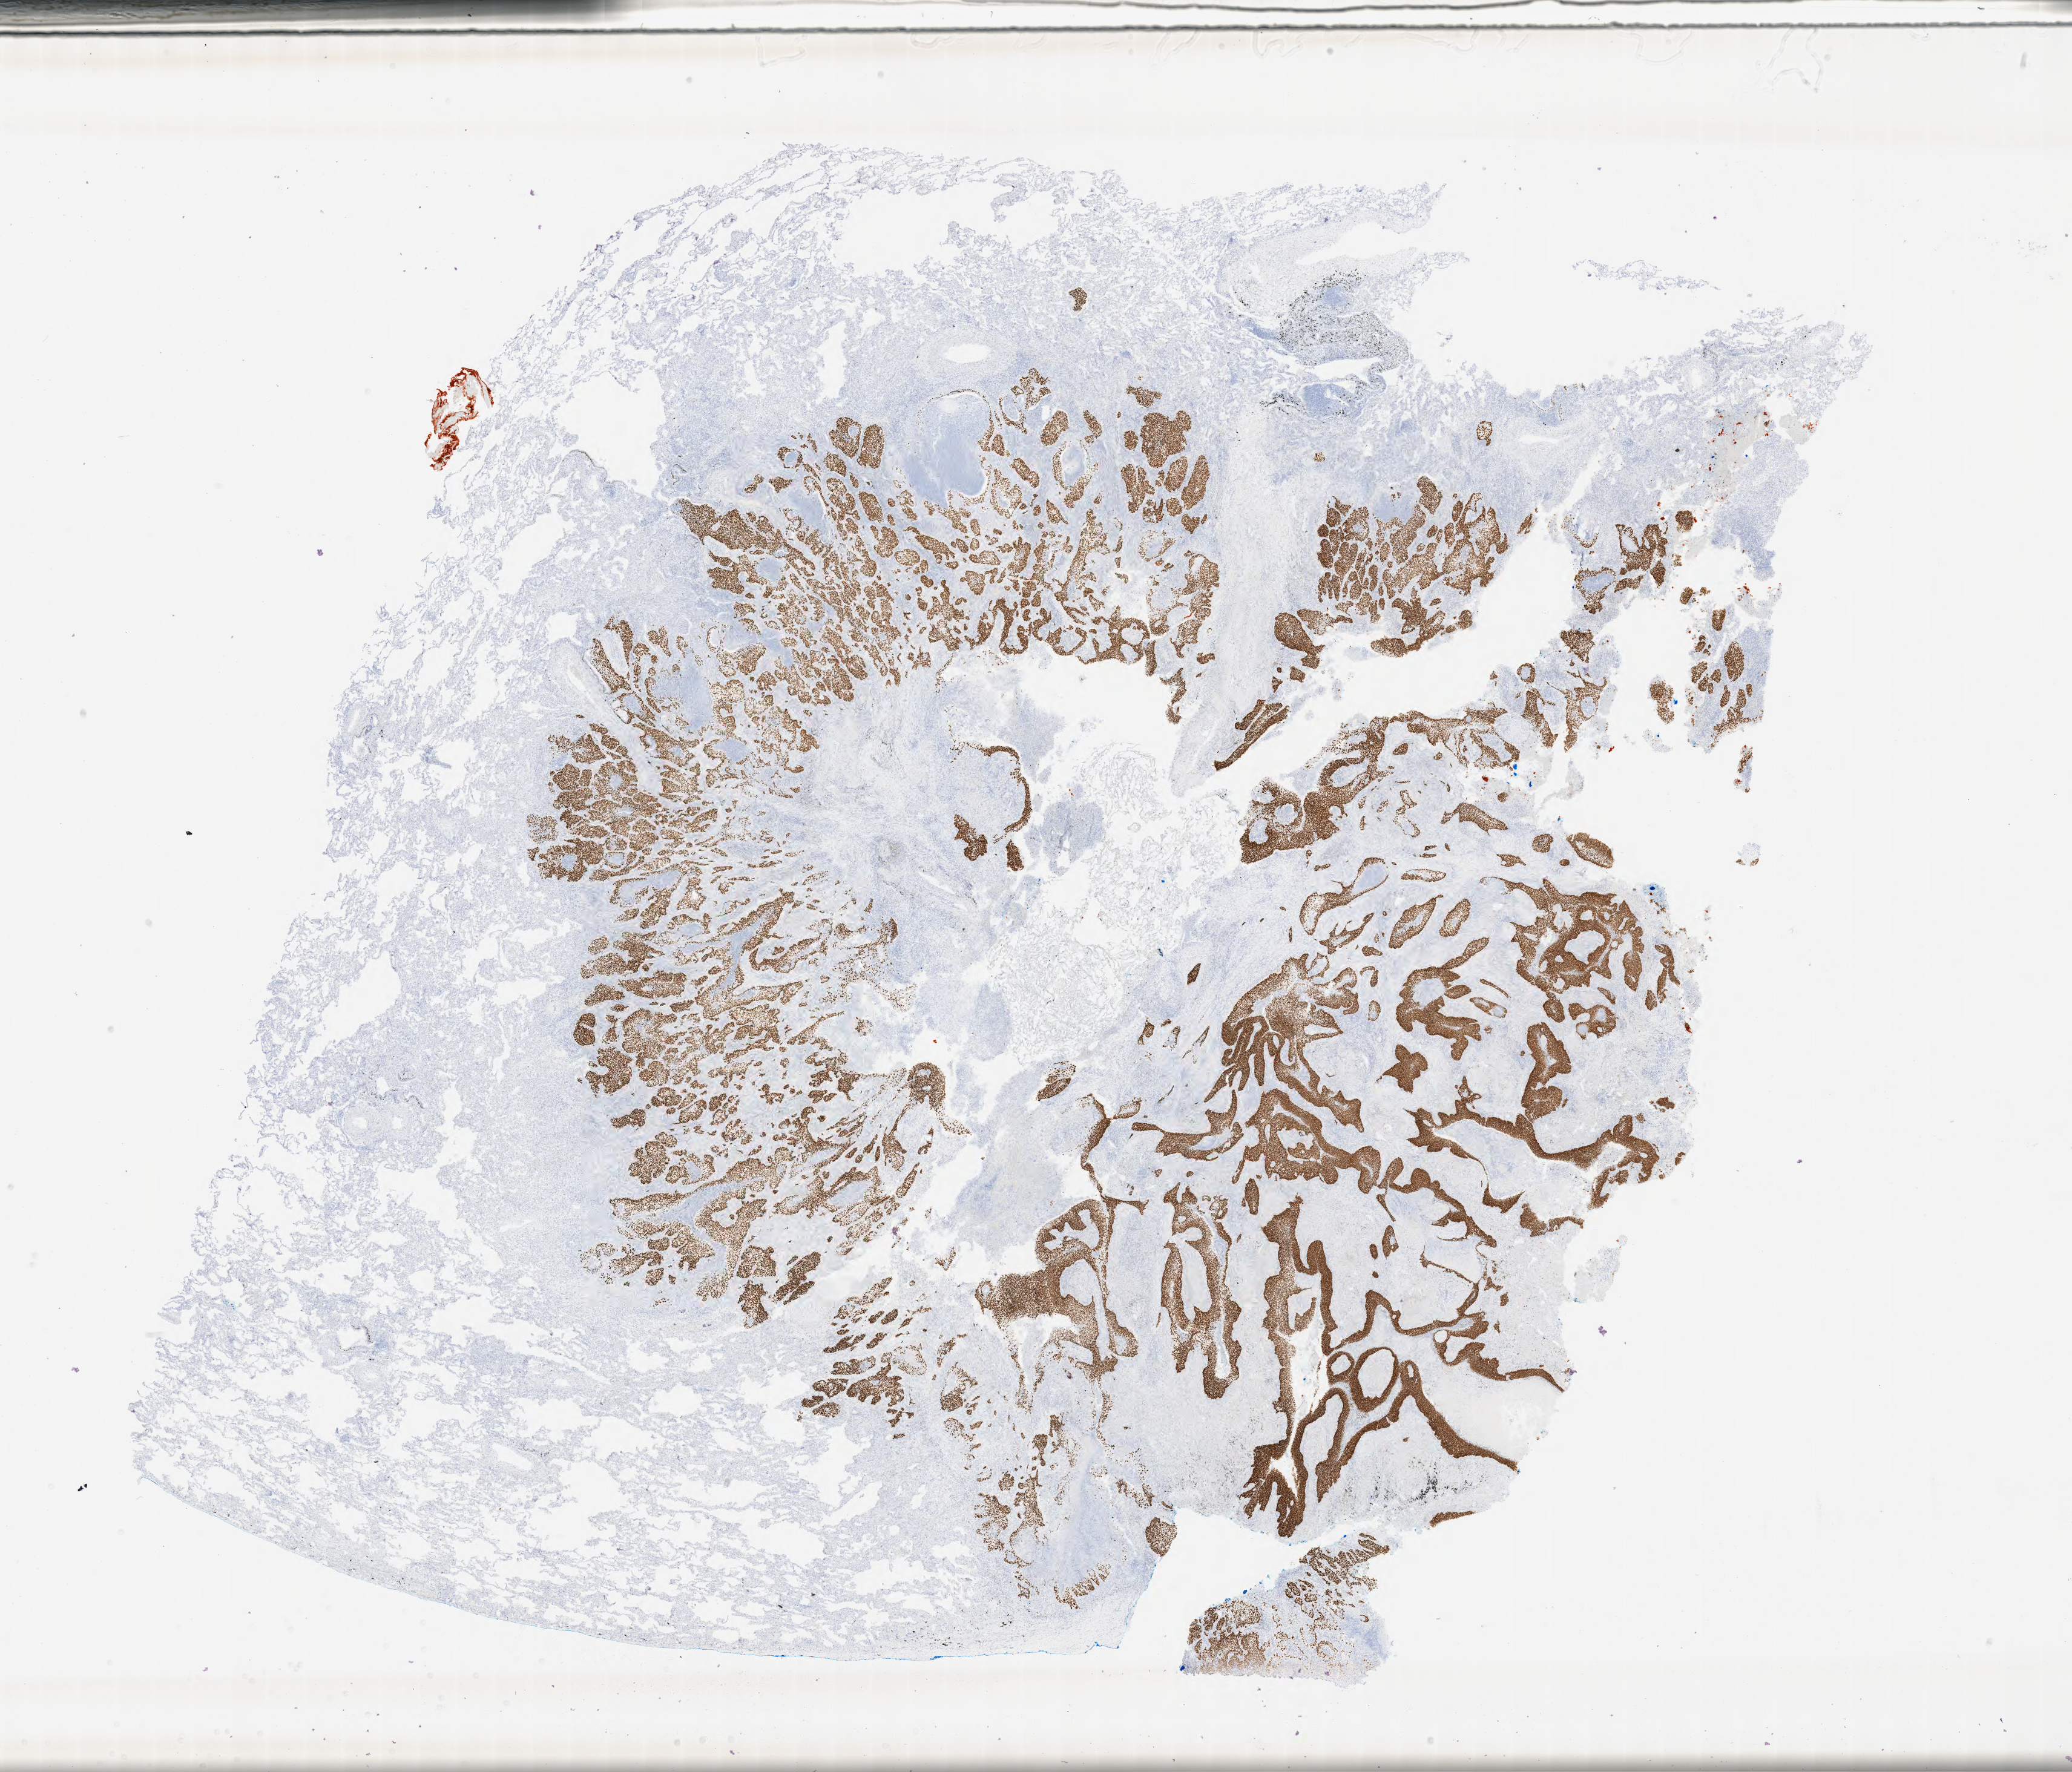
Immunohistochemistry (IHC) whole-slide image stained for p40 — a low-resolution overview of the entire scanned area, about 27.7 x 23.7 mm. Specimen: tumor tissue. Anatomic site: lung. Patient sex: male.
- diagnosis: Squamous cell carcinoma, NOS